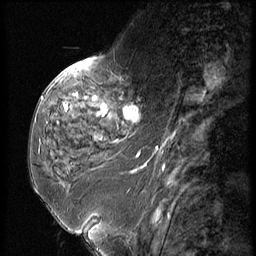
Breast MRI (dynamic contrast-enhanced), one sagittal slice; slice 21 of 56 in the series (ordered by position); dynamic contrast-enhanced series, image 2 of 3 at this slice position (ordered by acquisition); 1.5 T; TE 4.2 ms, TR 9 ms; 2.5 mm slice thickness; 256 × 256 image matrix, field of view 180 × 180 mm. Female patient, age 59 years. Case-level facts recorded for this patient, not image findings: setting: breast cancer imaged before/during neoadjuvant chemotherapy; receptor status: HER2-positive.
Outlined on this slice (semi-automatic segmentation, software-assisted and operator-edited):
- analysis volume of interest (the breast-tissue region the enhancement analysis was run in; not a lesion): box from (x=44, y=66) to (x=151, y=135) px
- tumour enhancement mask (voxels above the 140 % enhancement threshold inside the analysis volume of interest): (x=64, y=94)–(x=136, y=119)